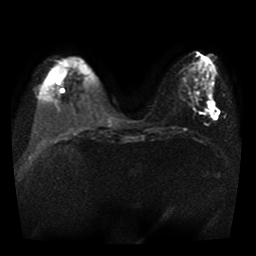
Breast MRI, one axial slice; position 13 of 41 along the scan axis; diffusion-weighted series; image 2 of 4 stored at this slice position (different b-values; order by instance number); 1.5 T; 5 mm slice thickness; 256 × 256 image matrix, field of view 330 × 330 mm. Female patient.
Structures marked on this image (outlined manually by an expert reader):
- tumour on diffusion-weighted imaging: box from (x=208, y=102) to (x=220, y=119) px